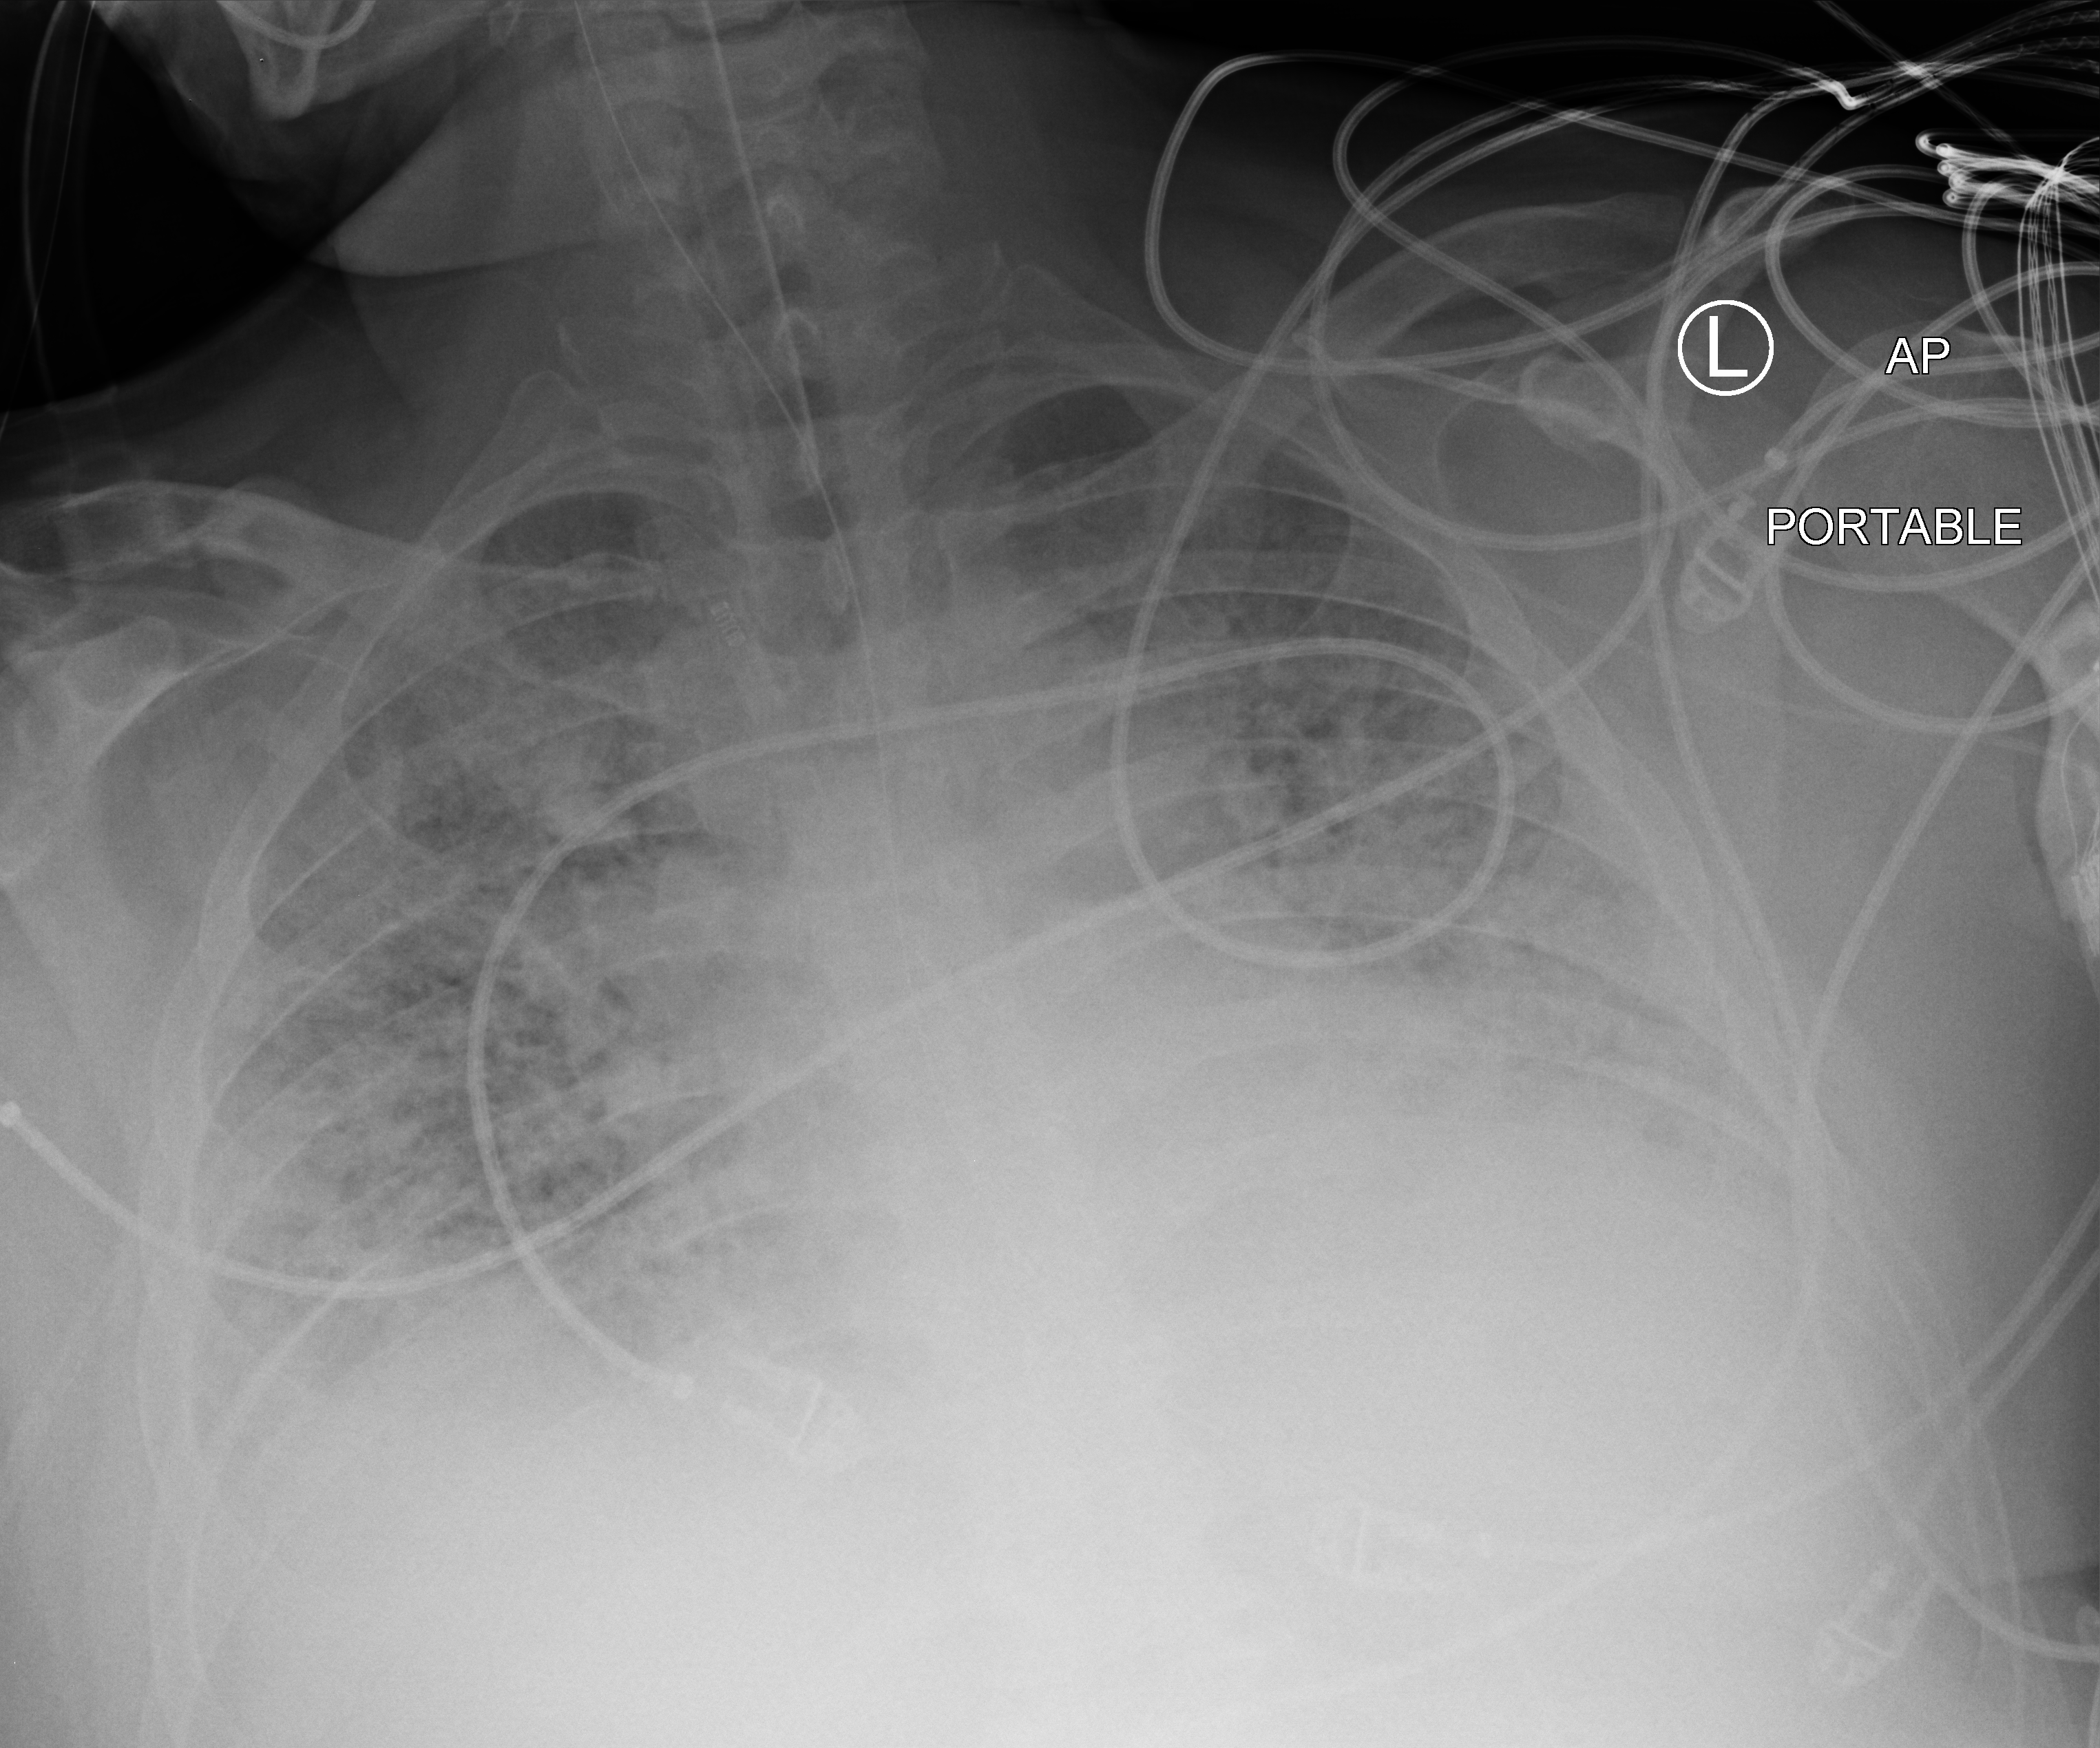
Chest X-ray (portable), anteroposterior (AP) projection. Patient hospitalised with COVID-19, aged 18–59 years.
Admission-level facts for this patient (not findings on this image; timing relative to this image not recorded):
- admitted to intensive care during this hospital stay: yes
- length of hospital stay: 31 days